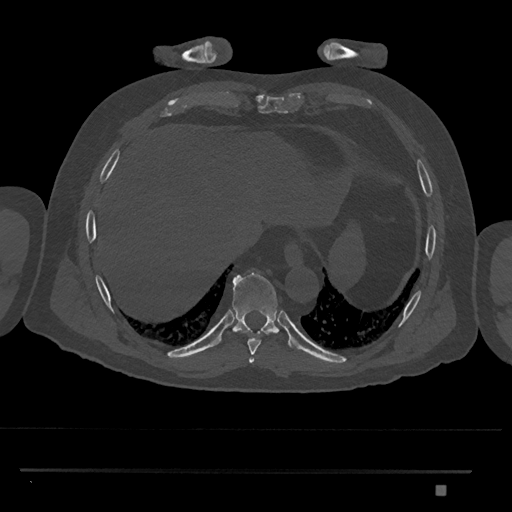
CT including the spine, one axial slice. Slice 1078 of 1134 in the series (ordered by position). Reconstruction kernel Br40s/3. 120 kVp. Bone window (W 1800 / L 400 HU). 0.5 mm slice thickness. 512 × 512 image matrix, field of view 429 × 429 mm. Male patient, age 65 years. From the clinical record (not read from this slice): primary cancer: prostate.
Structures marked on this image (semi-automatically segmented with operator editing):
- T8 vertebra: bounding box <248,333,268,355> (left, top, right, bottom; pixels)
- T9 vertebra: <220,270,290,346>